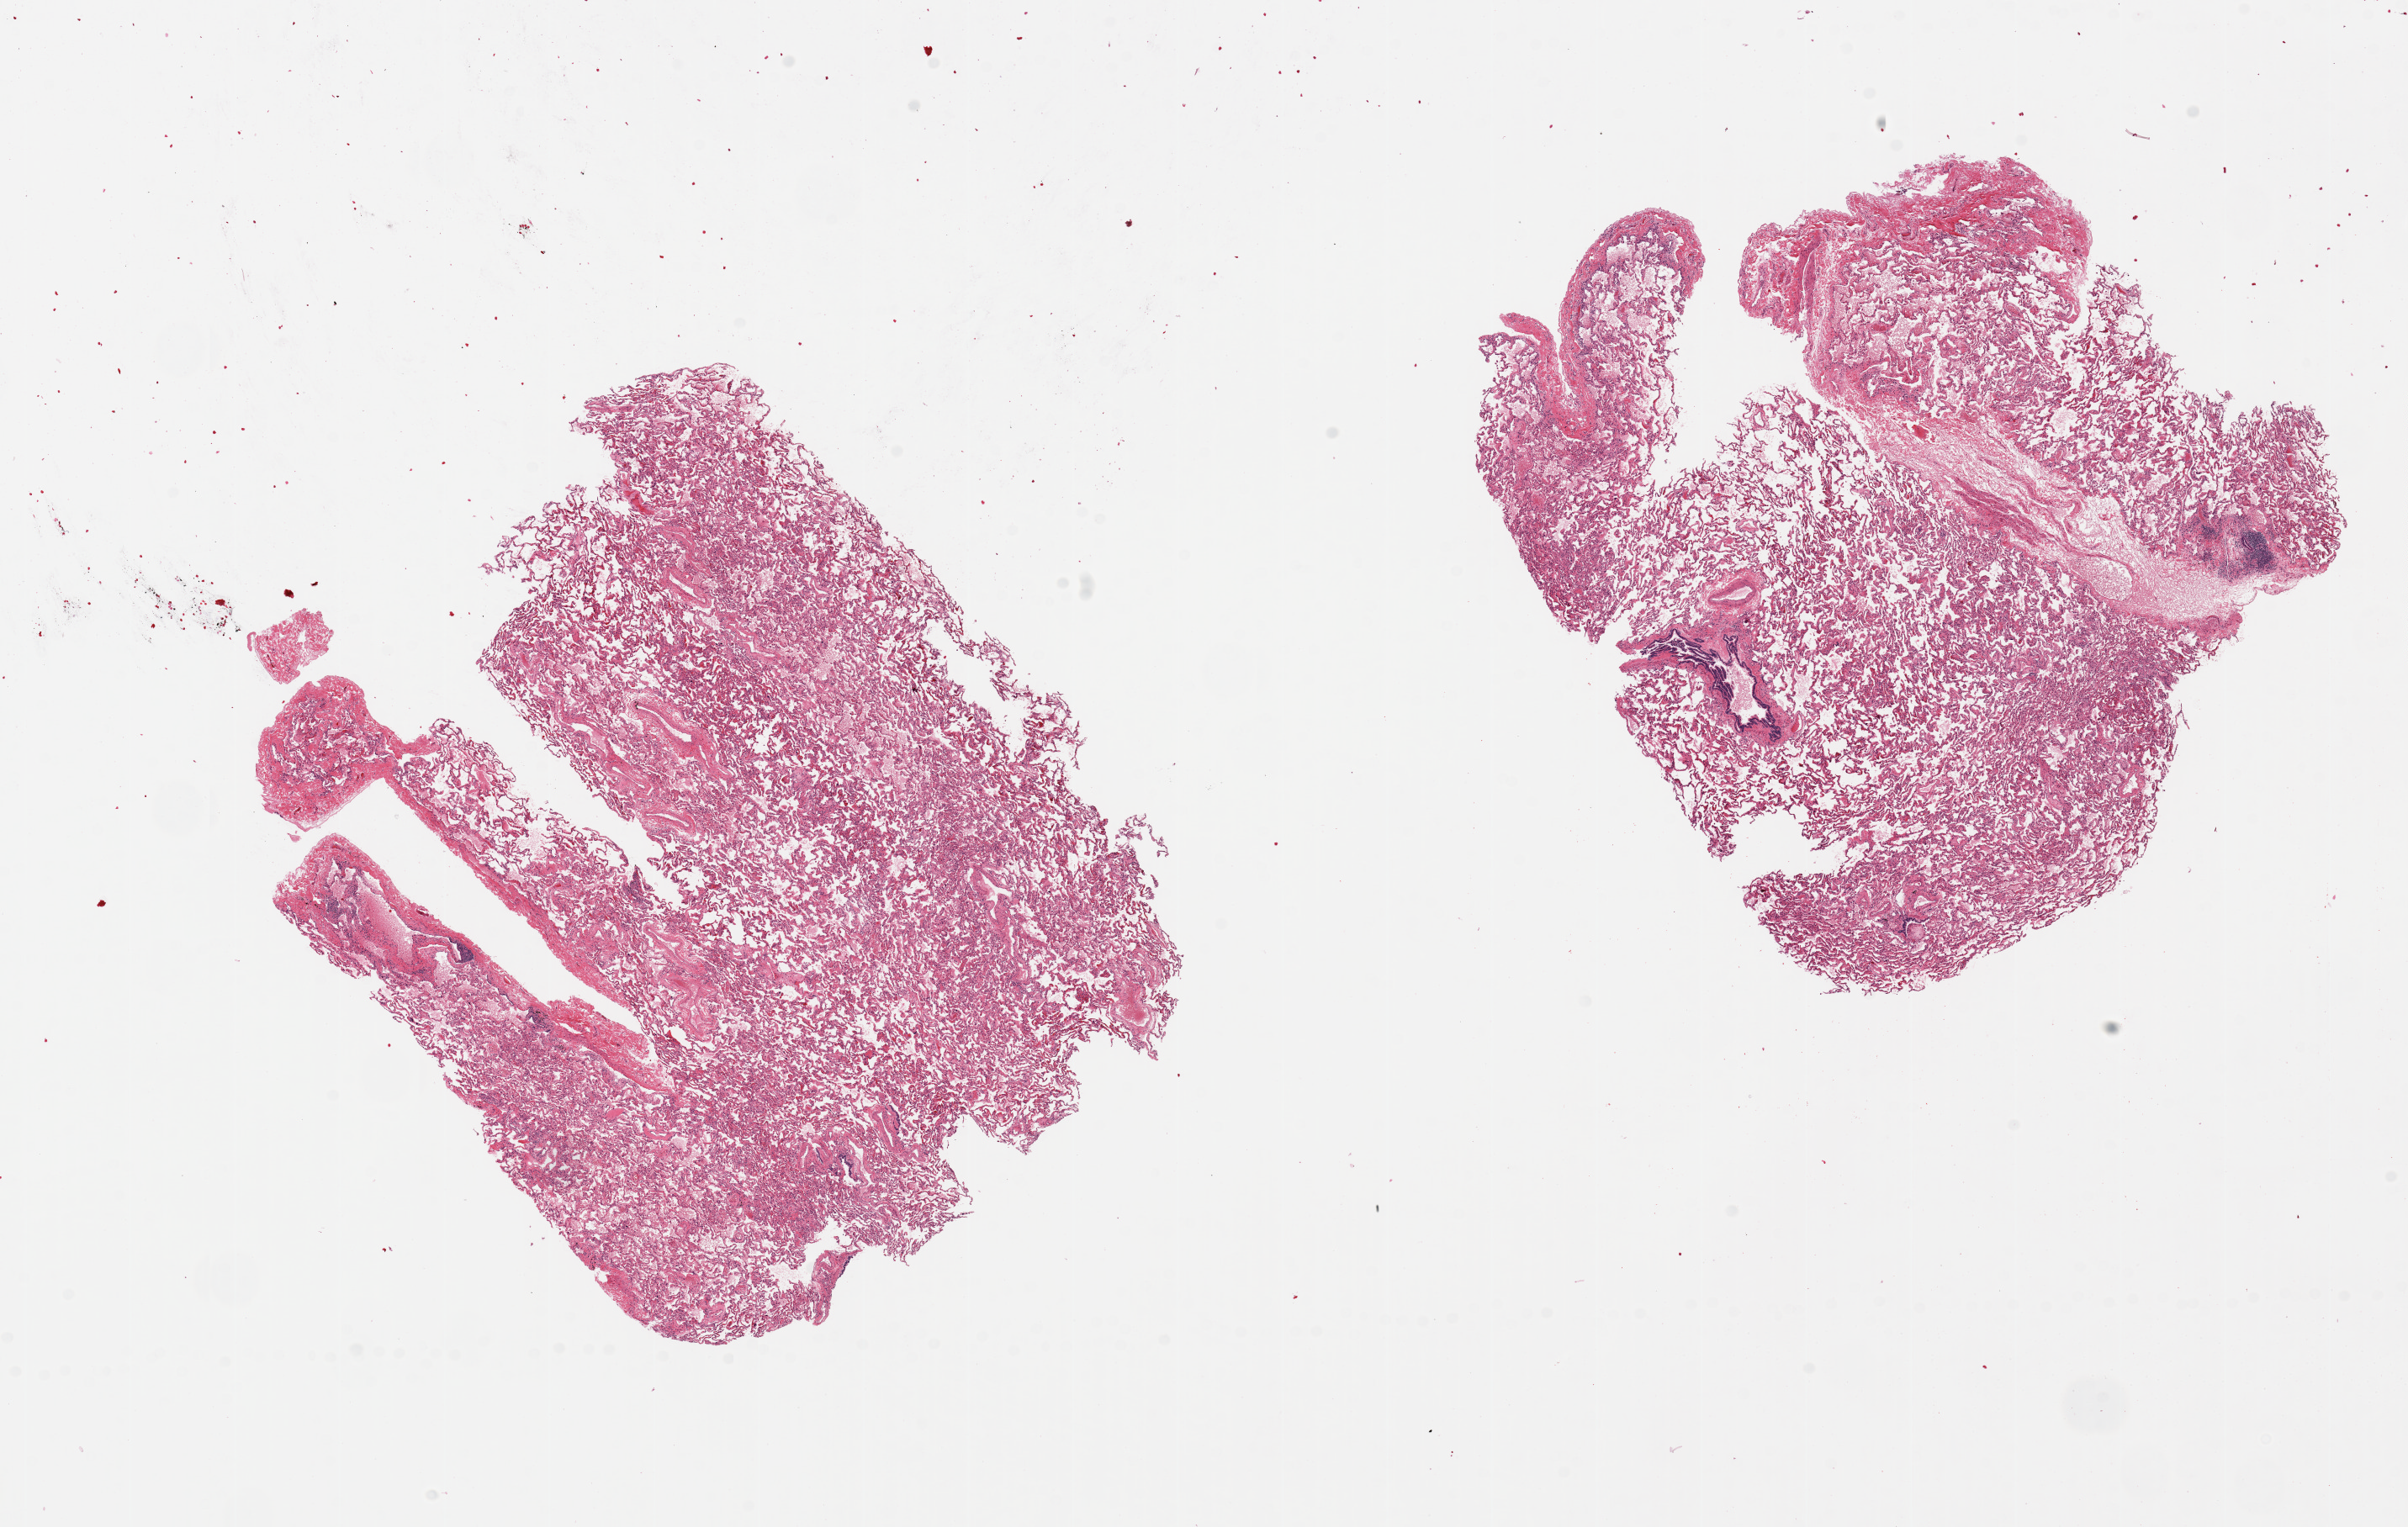
Whole-slide image, H&E stain, low-resolution overview of the scanned area, about 22.6 x 14.4 mm (acquisition: 20x scan). PAXgene-fixed paraffin-embedded (PFPE) section. Target tissue: lung. Tissue donor sample. Donor sex: male.
Pathologist's review note for this sample: 2 pieces, congestion, pigmented alveolar macrophages, some septal fibrosis and focal chronic inflammation.